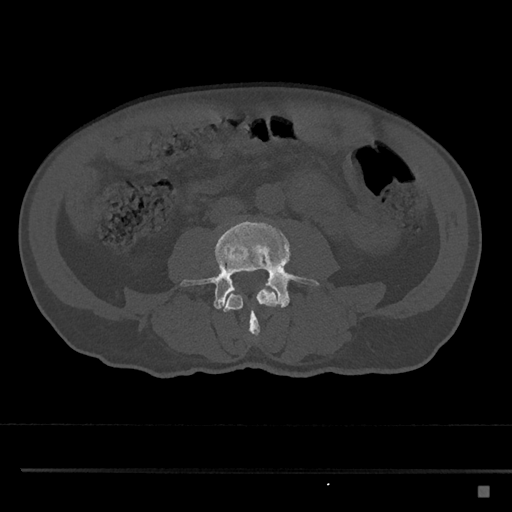
CT including the spine, one axial slice. Position 659 of 797 along the scan axis. Reconstruction kernel Br40s/3. Bone window (W 1800 / L 400 HU). 0.5 mm slice thickness. 512 × 512 image matrix, field of view 391 × 391 mm. Patient: male, 59 years. Case-level facts recorded for this patient, not image findings: primary cancer: prostate.
Outlined on this slice (semi-automatically segmented with operator editing):
- L3 vertebra: bounding box <222,283,282,336> (left, top, right, bottom; pixels)
- L4 vertebra: <180,221,320,309>